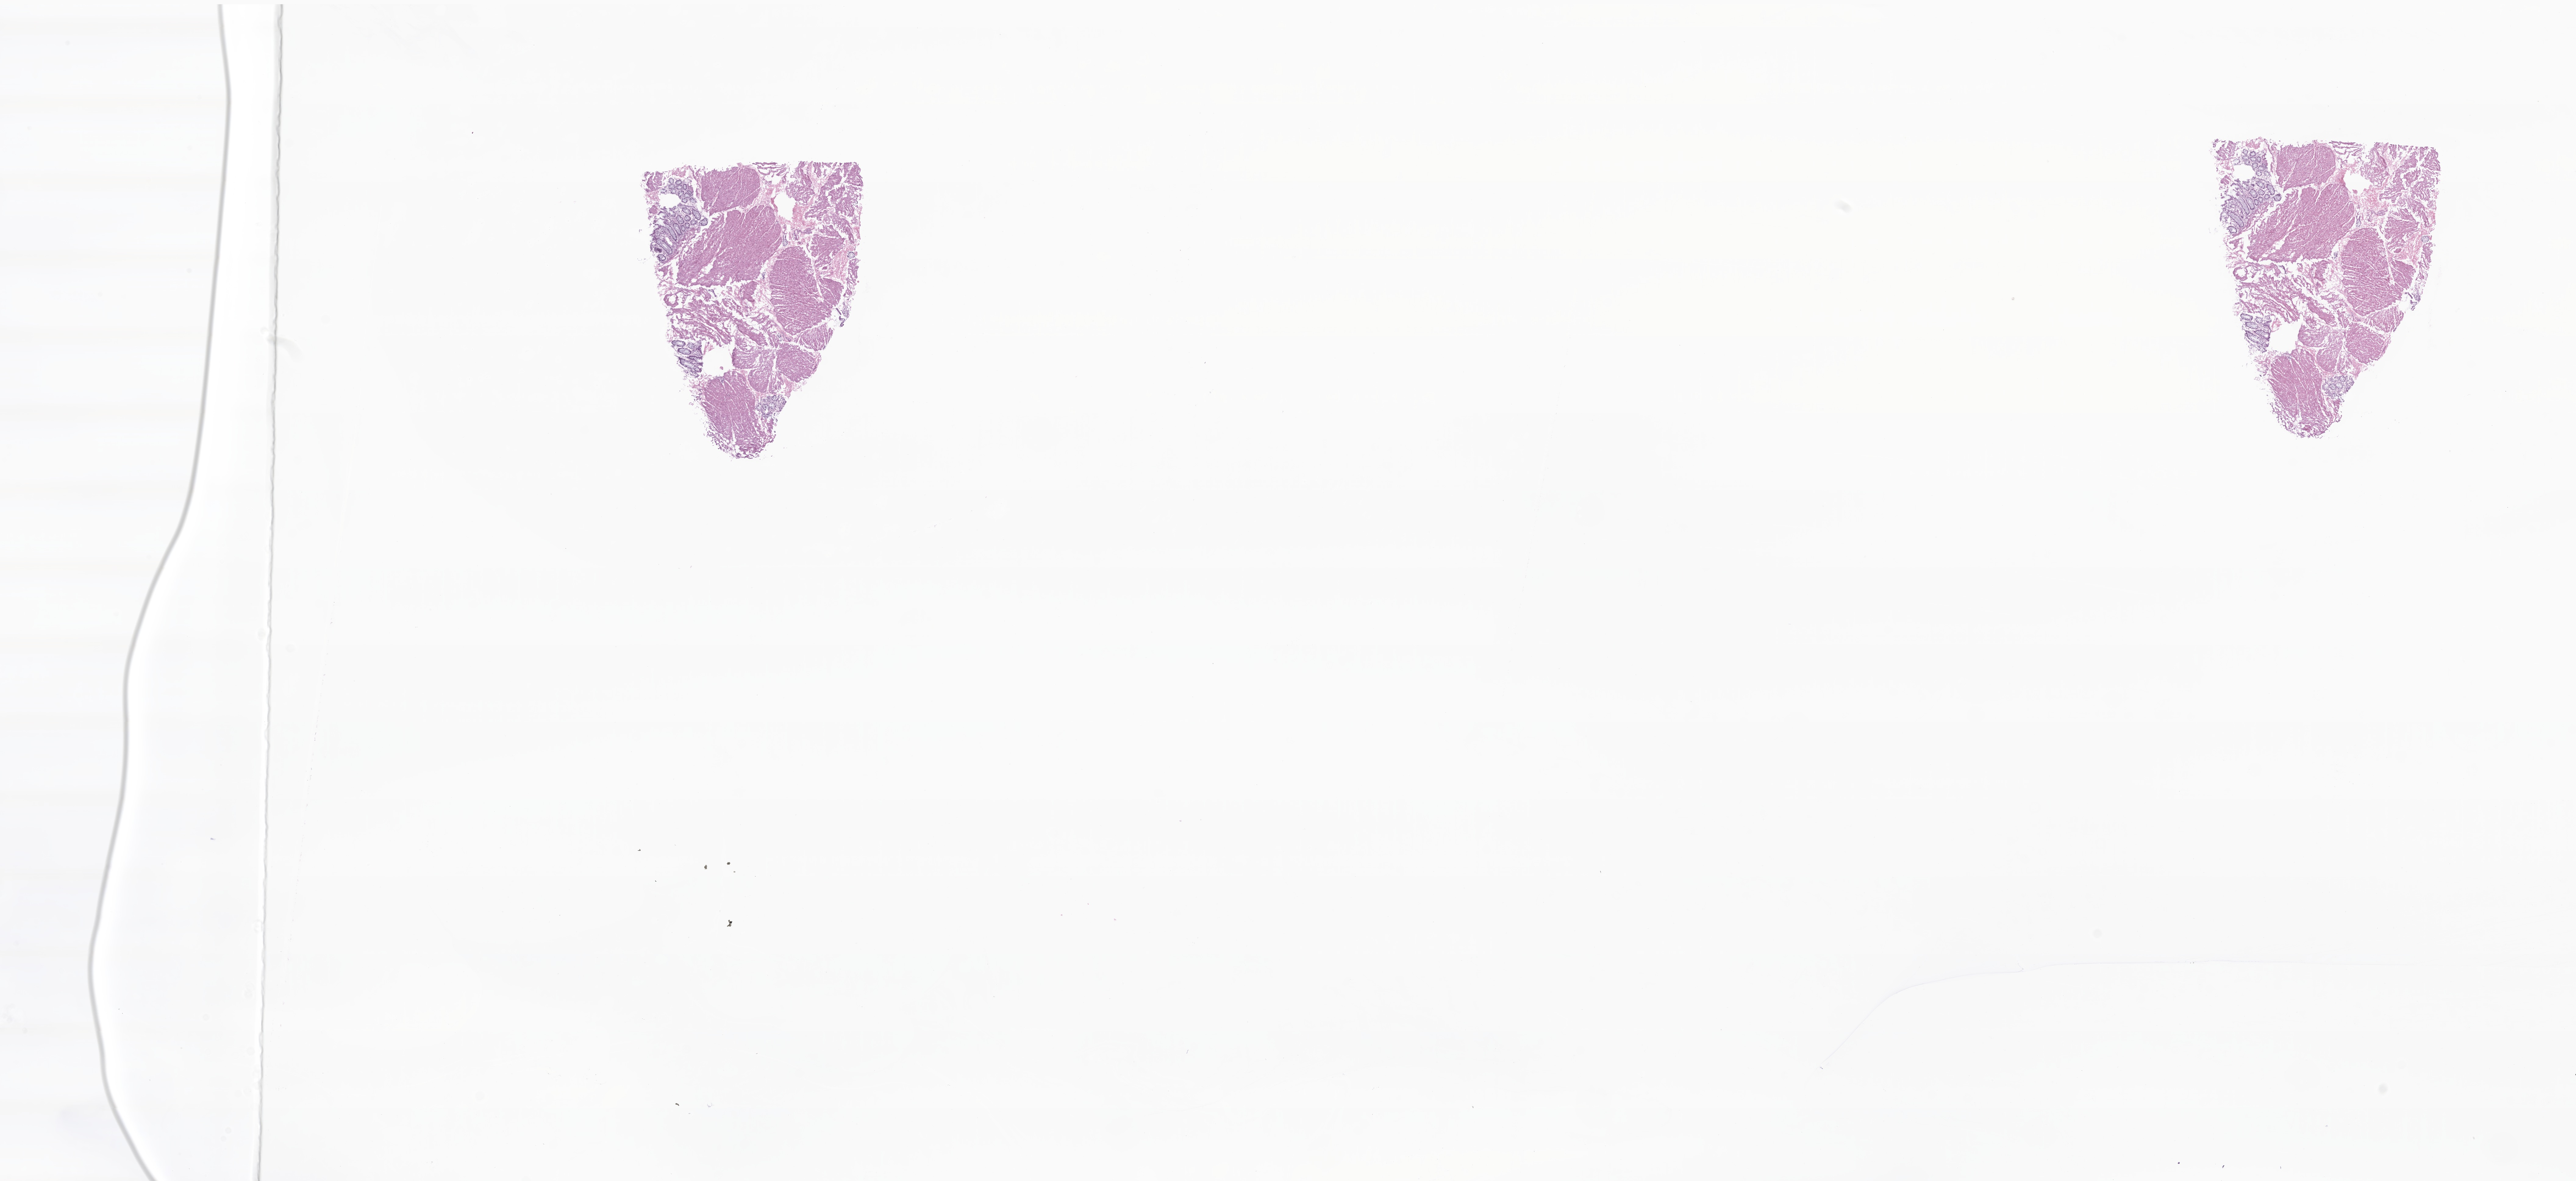
Digitized hematoxylin and eosin (H&E)-stained section — shown as a low-resolution overview of the whole scanned area (about 35.6 x 16.3 mm), cryosection, specimen: non-tumor (normal tissue) sample from a patient with adenocarcinoma, NOS, anatomic site: rectosigmoid junction. Female patient. Slide review estimates, as recorded: tumor cells 0%, tumor nuclei 0%, stromal cells 0%, necrosis 0%, normal cells 100%. Infiltration values recorded for this section: lymphocyte infiltration 0%, monocyte infiltration 0%, neutrophil infiltration 0%.
This section: non-tumor tissue sample; the patient's diagnosis is given above. Section: top of the tissue portion.